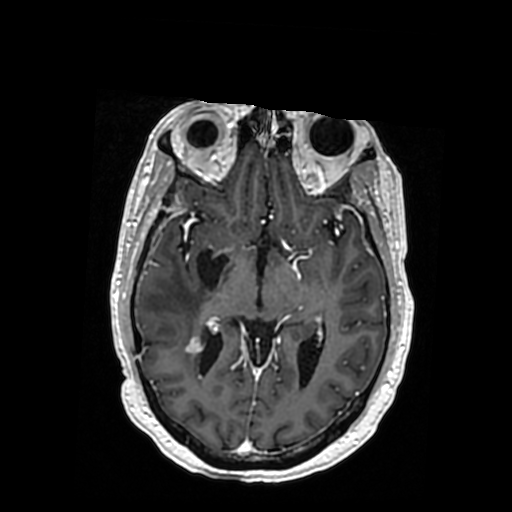
Brain MRI from a brain-tumour surgery series, one axial slice. Slice 198 of 364 in the series (ordered by position). T1-weighted post-contrast. 0.5 mm slice thickness. 512 × 512 image matrix, field of view 260 × 260 mm. Case-level facts recorded for this patient, not image findings: histopathology: Oligodendroglioma; WHO grade: 3; IDH mutation: yes; tumour location: Right Posterior Temporal Inferior Parietal.
Outlined on this slice (outlined manually by an expert reader):
- previous resection cavity: bounding box [x1, y1, x2, y2] px = [197, 250, 228, 289]
- tumour: [189, 334, 206, 348]